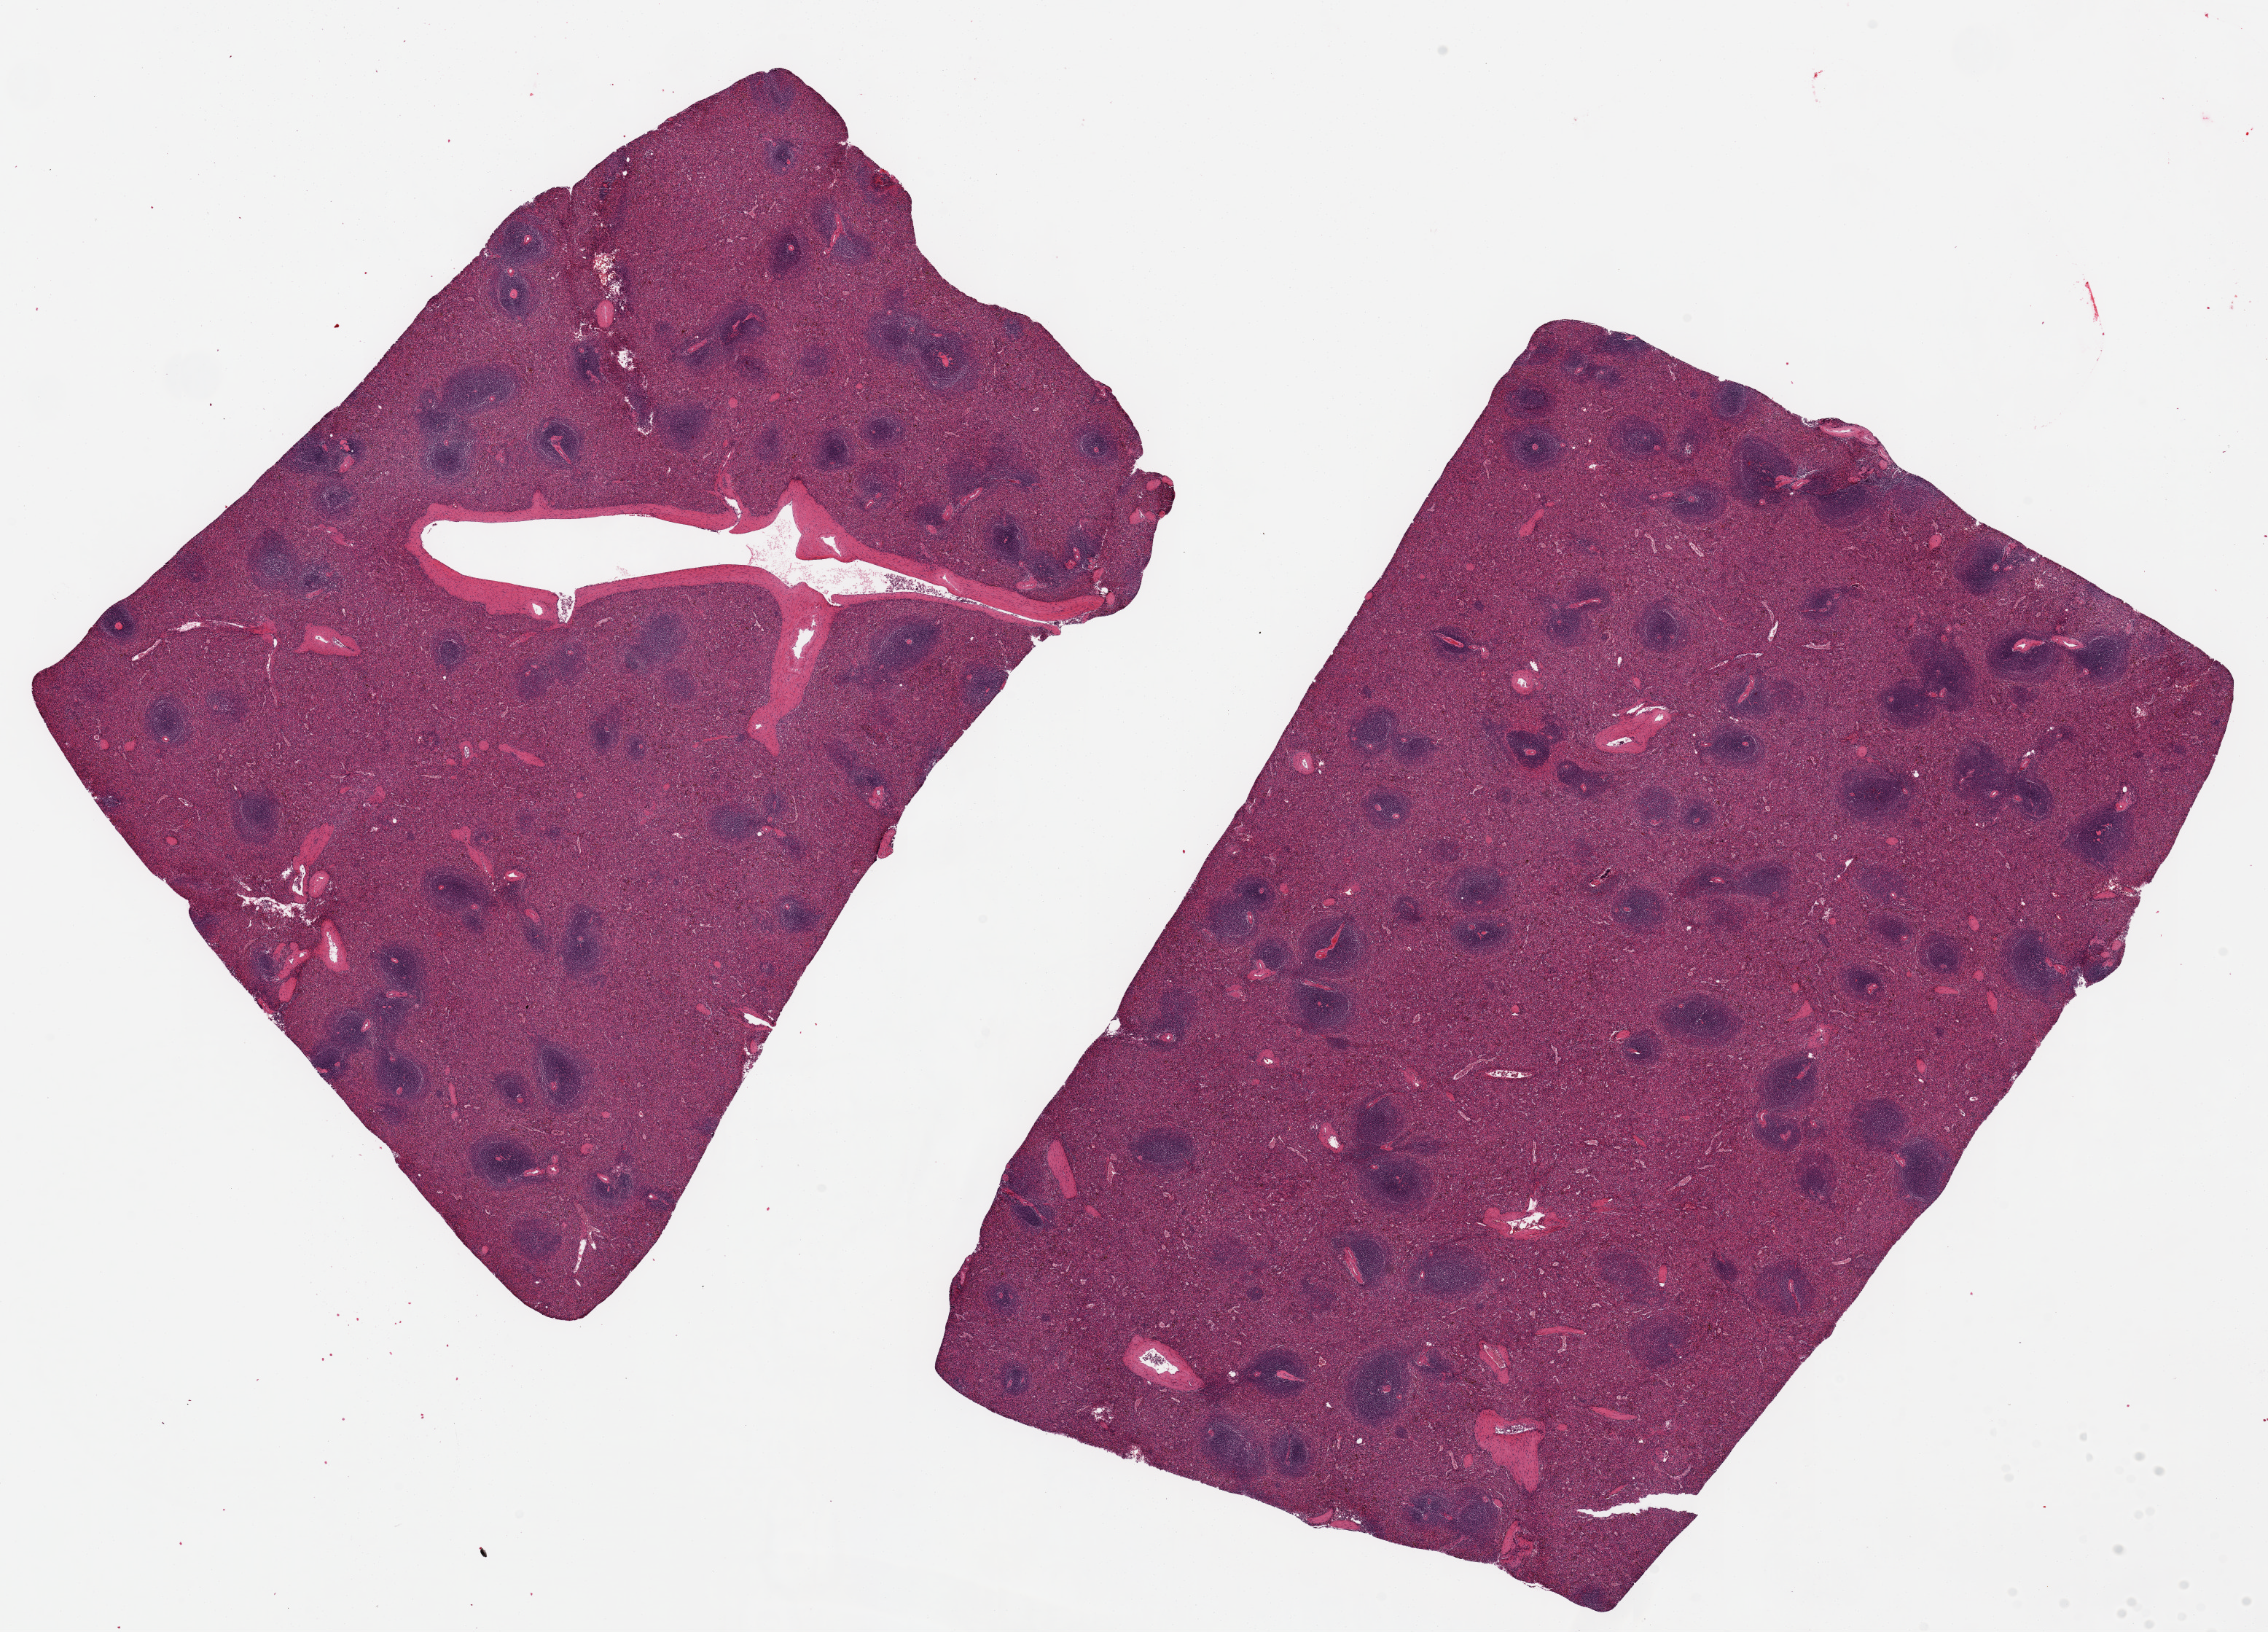
Digitized haematoxylin and eosin-stained section, low-resolution overview of the scanned area, about 24.6 x 17.7 mm (from a 20x scan). PAXgene-fixed paraffin-embedded (PFPE) section. Section of spleen (target tissue). Tissue donor sample. Donor sex: male.
Review note (as recorded): 2 ~12x9mm aliquots. Reasonably well-preserved.